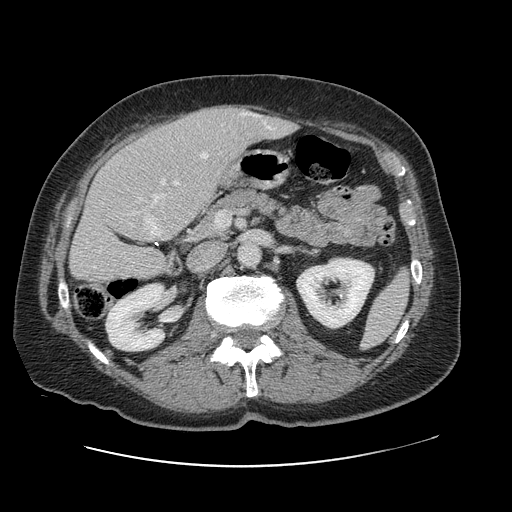
Contrast-enhanced abdominal CT, one axial slice; slice 44 of 138 in the series (ordered by position); 120 kVp; intravenous contrast given; soft-tissue window (W 400 / L 40 HU); 2.5 mm slice thickness; 512 × 512 image matrix, field of view 402 × 402 mm. Male patient, age 71 years. Case-level facts recorded for this patient, not image findings: diagnosis: colorectal cancer liver metastases, imaged before liver resection; multiple liver metastases: no; largest metastasis: 3.3 cm; chemotherapy before resection: no.
Structures marked on this image (expert manual segmentation):
- hepatic veins: bounding box (x1, y1, x2, y2) in pixels: (94, 113, 272, 268)
- liver: (71, 106, 295, 282)
- planned liver remnant (the part of the liver to remain after resection): (71, 137, 195, 283)
- portal vein (with intrahepatic branches): (161, 180, 165, 184)